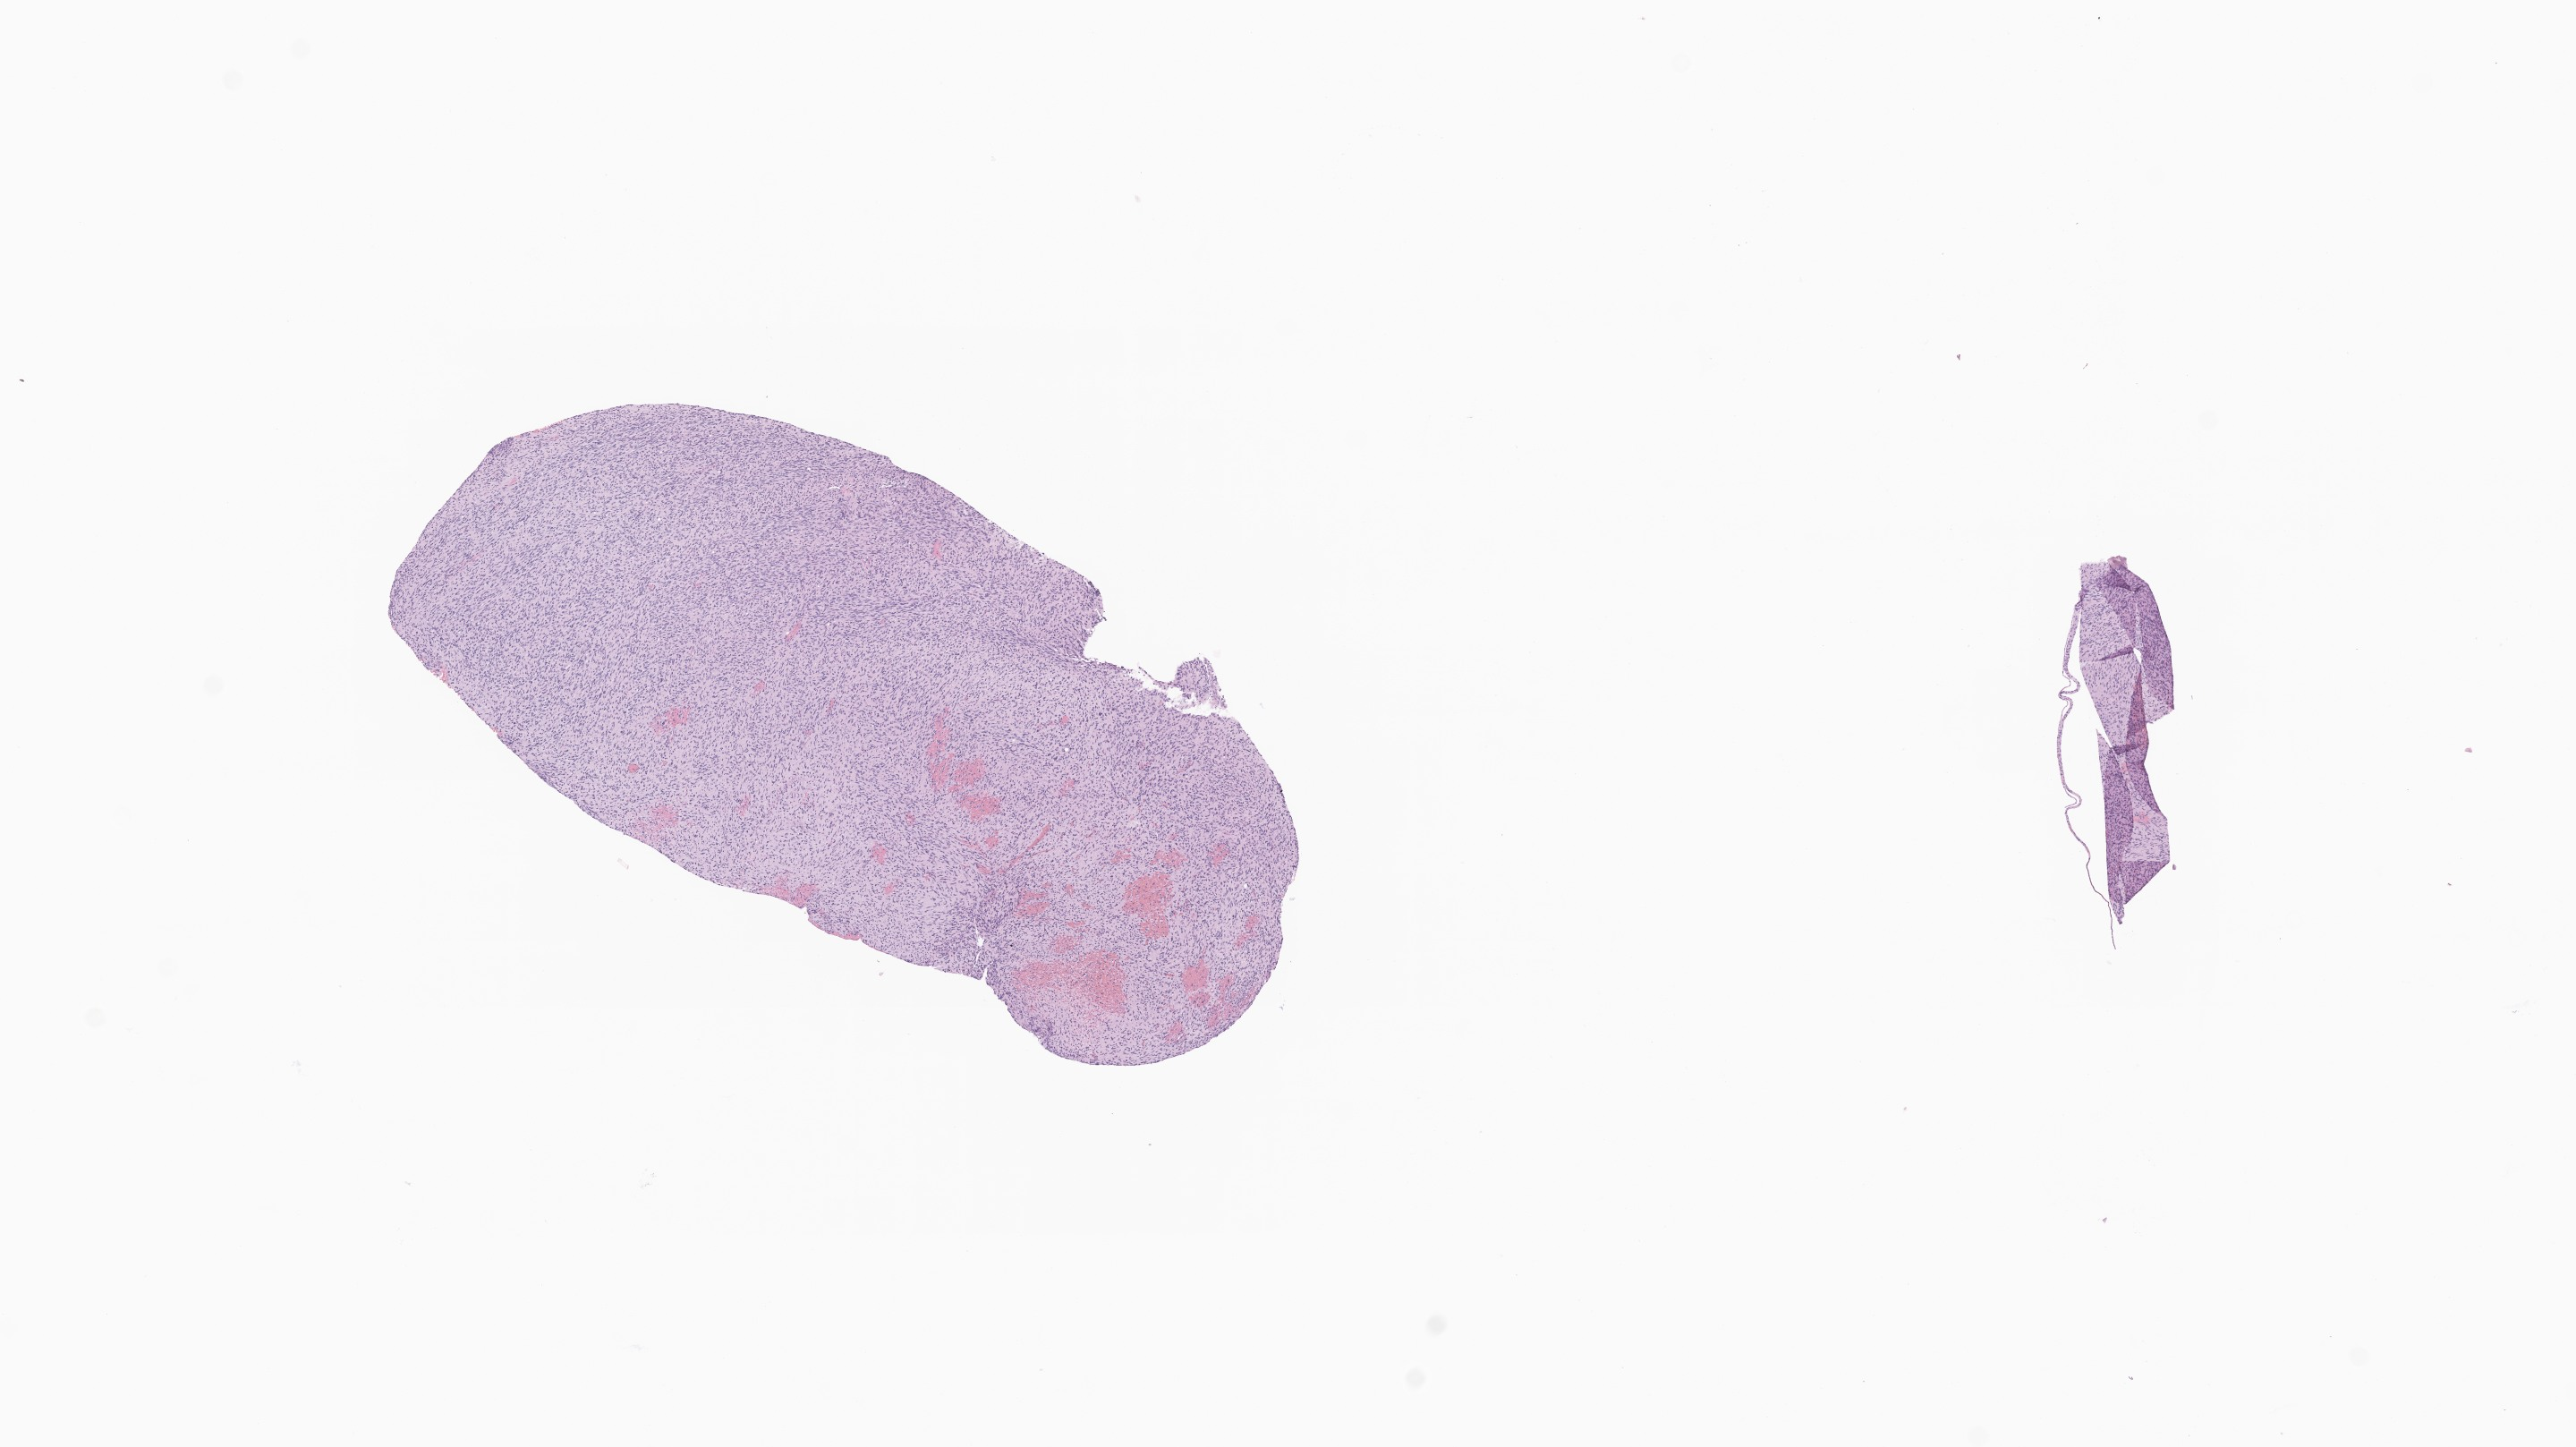
Whole-slide image, H&E stain of tumor tissue from the brain, shown as a low-resolution overview of the whole scanned area (about 12.1 x 6.8 mm); formalin-fixed, paraffin-embedded (FFPE) tissue. Patient: female, age 130 months (10 years 10 months).
Recorded diagnosis: Glioma, malignant.